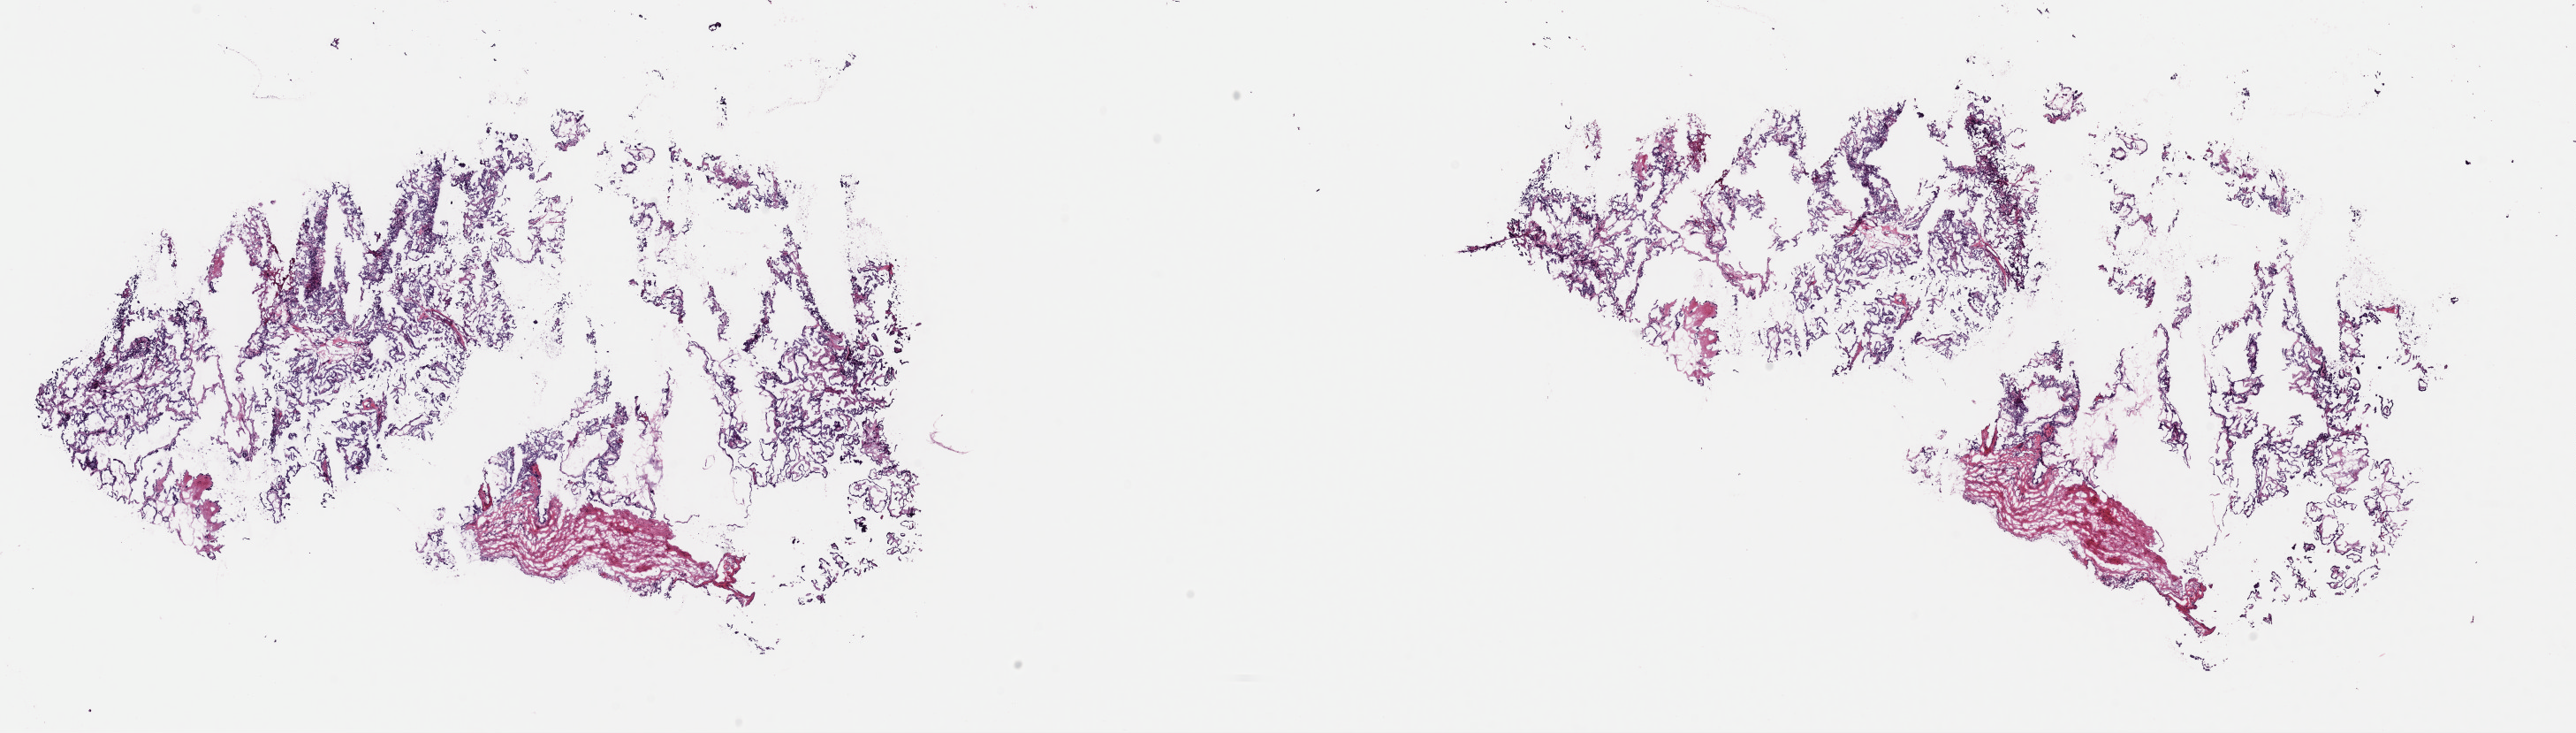
Hematoxylin and eosin (H&E) stained whole-slide image, a low-resolution overview of the entire scanned area, about 23.0 x 6.5 mm, frozen section from the top of the tissue portion, sample: primary tumour, thyroid. Female patient; age at initial diagnosis 36 years. Pathologist review of this section (percent, as recorded): tumour cells 95%, tumour nuclei 85%, normal cells 0%, stromal cells 5%, necrosis 0%. Infiltration values recorded for this section: lymphocyte infiltration 0%, monocyte infiltration 0%, neutrophil infiltration 0%.
* histologic diagnosis: Papillary adenocarcinoma, NOS (thyroid gland)
* AJCC pathologic stage: I (6th edition)
* lymph nodes positive (case pathology): 3 of 11 examined
* laterality: right